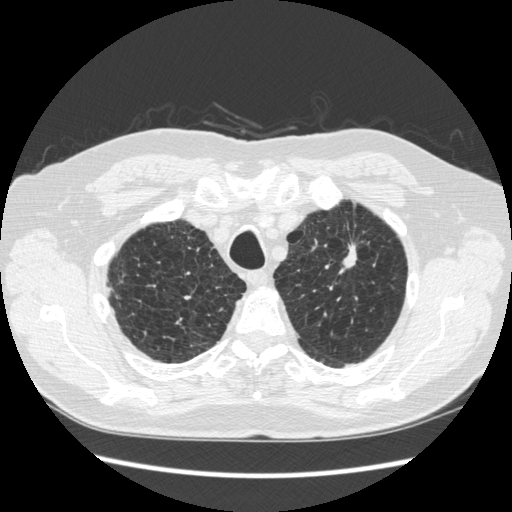
Chest CT (low-dose screening protocol), one axial image; third annual screen; lung window (W 1500 / L -600 HU); 1.25 mm slice thickness; 512 × 512 image matrix. Male, age 70 years at enrolment. Former smoker at enrolment.
- Expert-annotated lung lesion, bounding box [x1, y1, x2, y2] px = [323, 221, 375, 286].
- The screening reader recorded 2 non-calcified nodules or masses ≥4 mm on this exam (left upper lobe, right lower lobe); which of them this box marks is not recorded.
- Later outcome: lung cancer diagnosed 92 days after this screen — squamous cell carcinoma, NOS, left upper lobe, moderately differentiated (G2), stage IA (AJCC 6th edition), 18 mm at pathology.